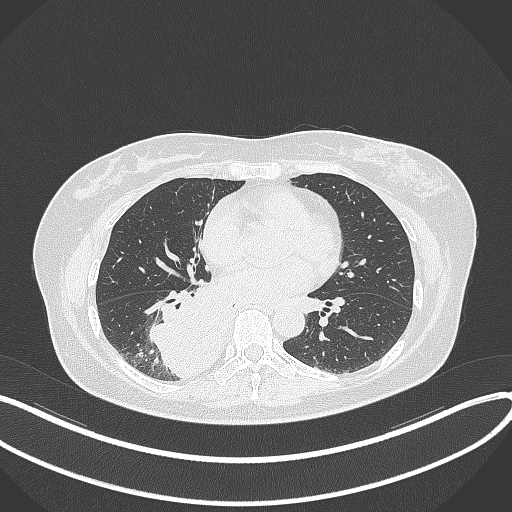
Chest CT, one axial slice. Position 162 of 331 along the scan axis. Reconstruction kernel B70f. 120 kVp. Lung window (W 1500 / L -600 HU). 1 mm slice thickness. 512 × 512 image matrix. Patient: female, 54 years. From the clinical record (not read from this slice): clinical TNM (as recorded): T4 N0 M0.
Structures marked on this image (bounding box drawn by a radiologist):
- lung tumour (recorded histology: adenocarcinoma): box from (x=145, y=292) to (x=223, y=385) px